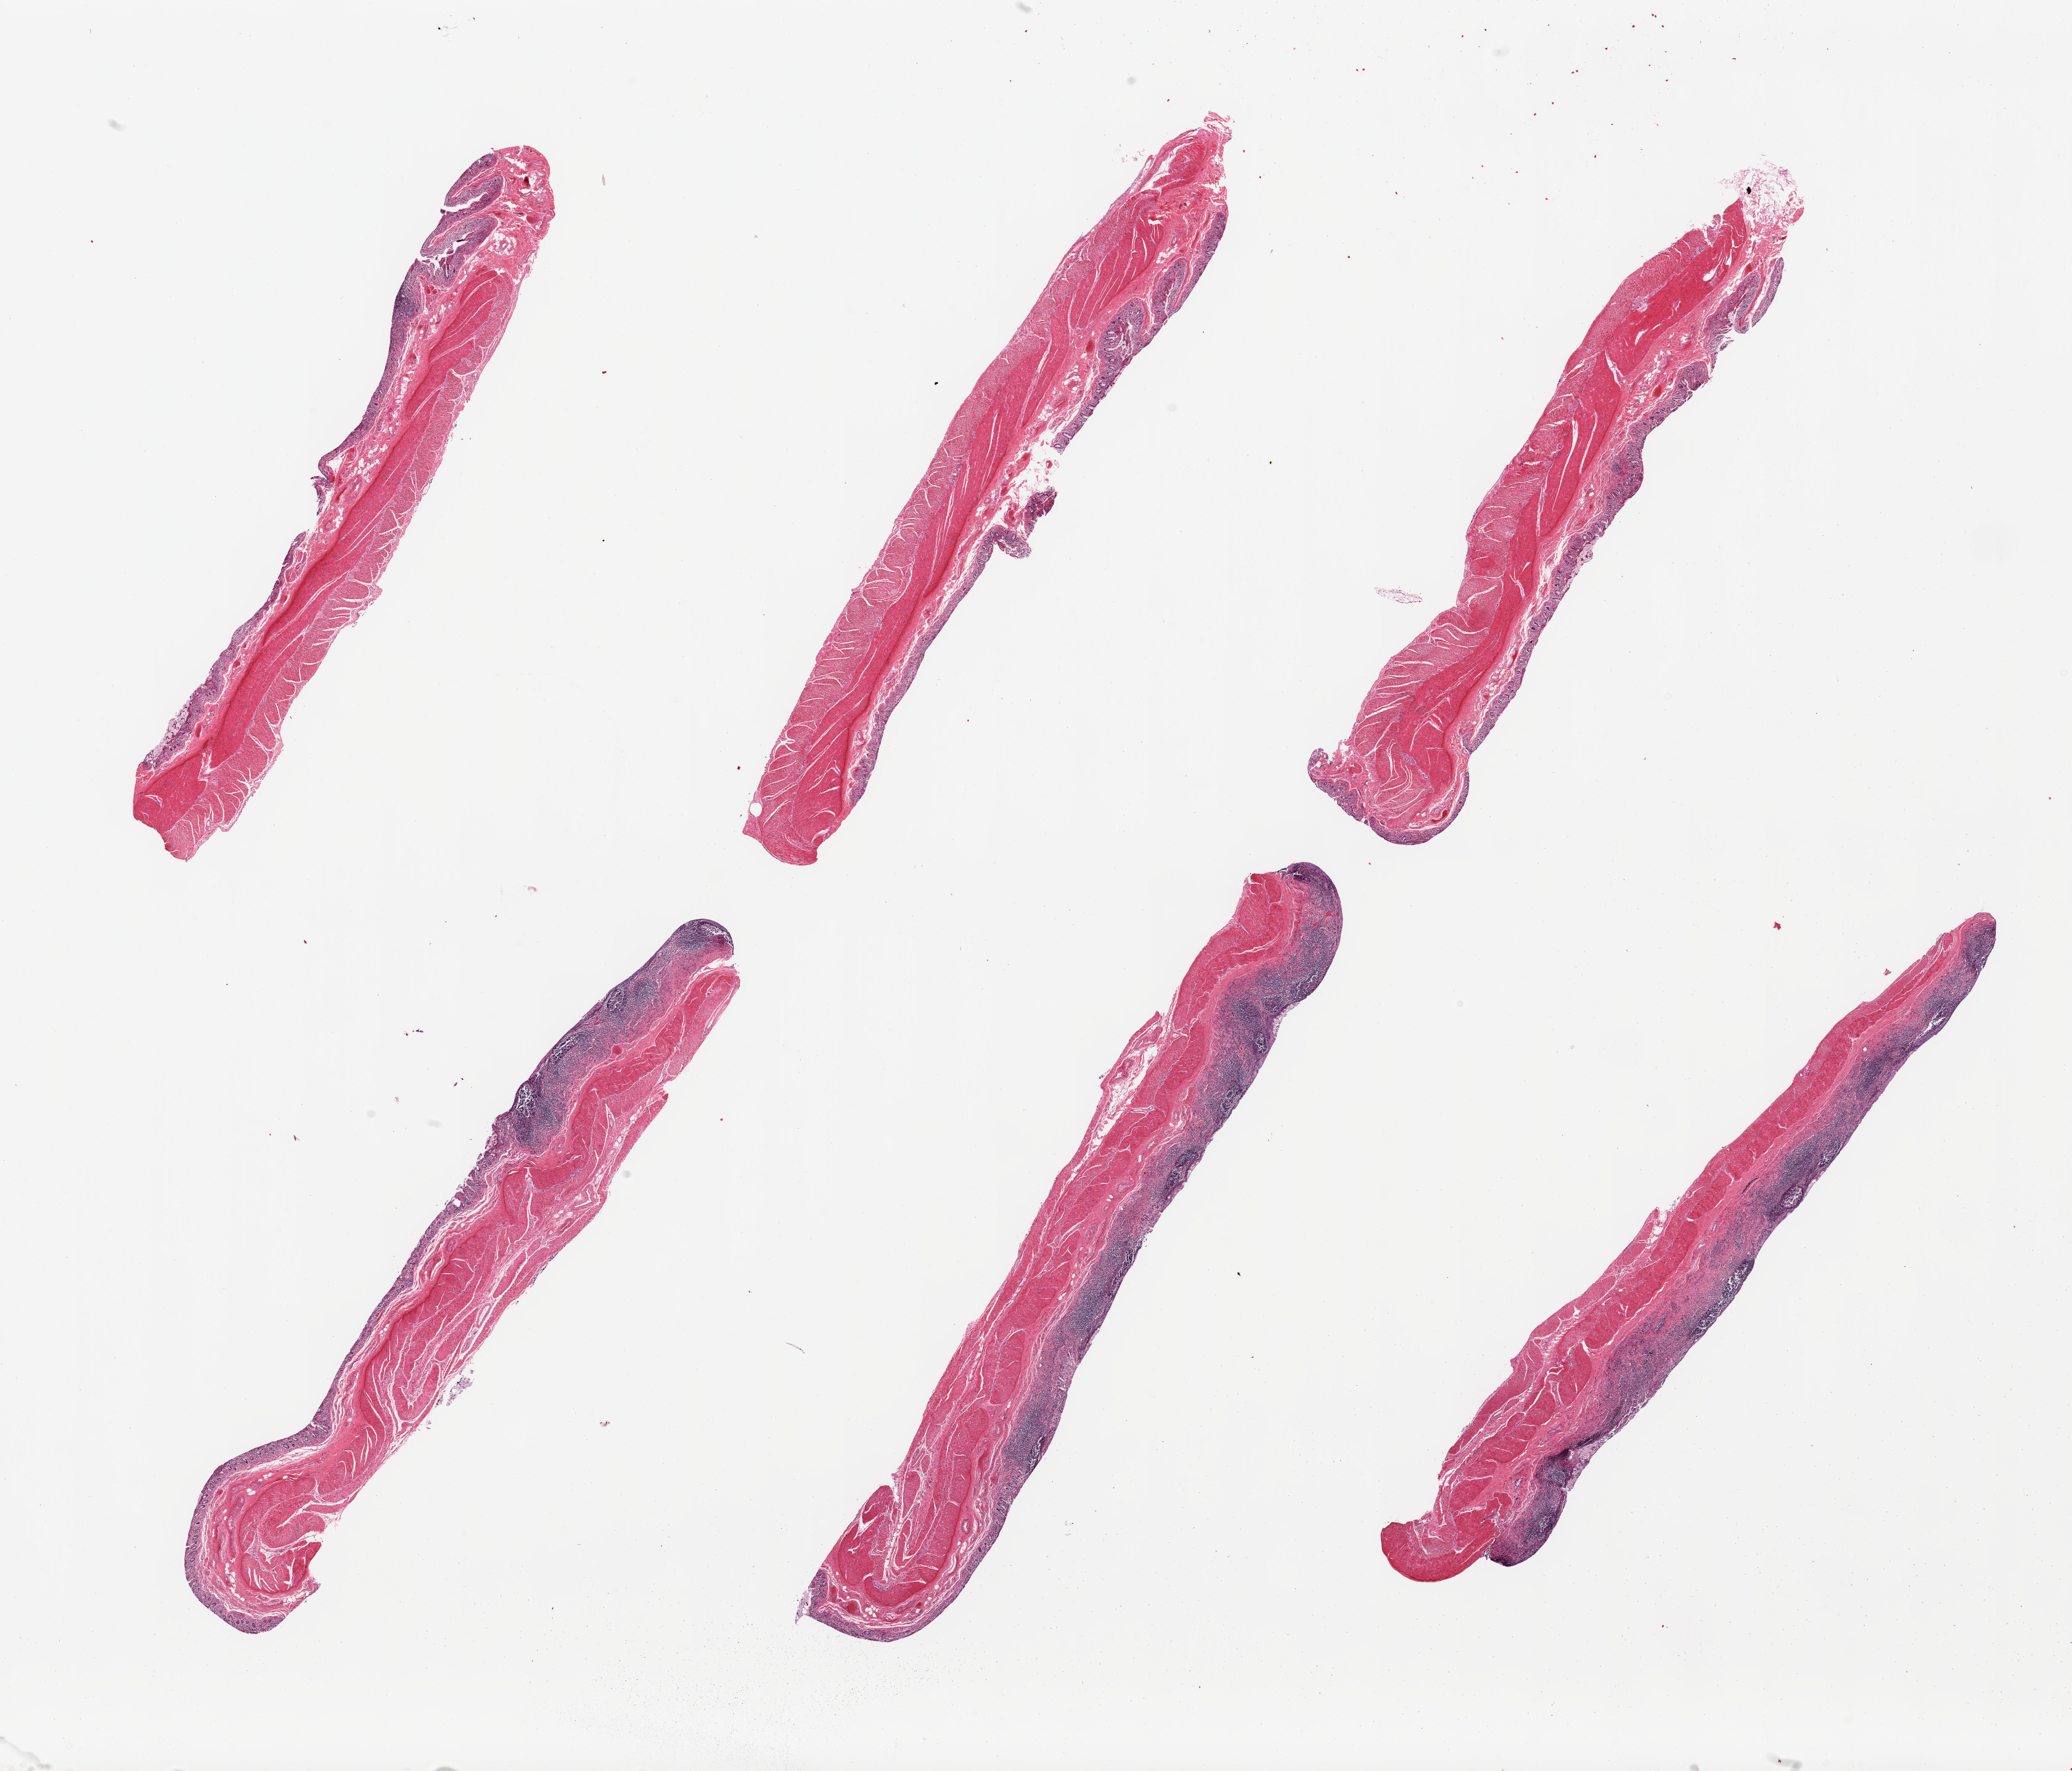
Haematoxylin and eosin whole-slide image, brightfield, shown as a low-resolution overview of the whole scanned area (about 26.6 x 22.7 mm, from a 20x scan).
- specimen: PAXgene-fixed, paraffin-embedded tissue; target tissue: ileum; tissue donor sample